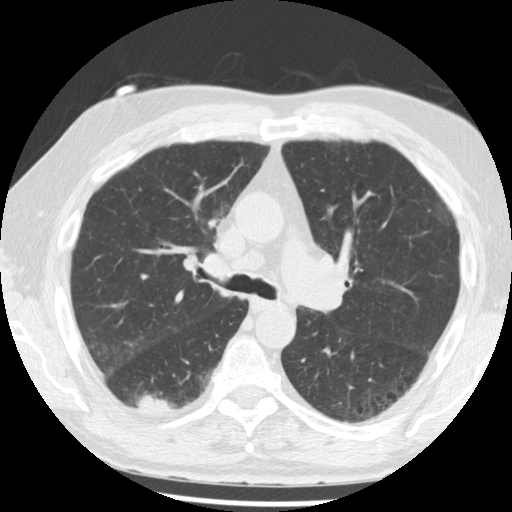
Axial slice from a low-dose chest CT screening exam; third screening round (two years after baseline); lung window (W 1500 / L -600 HU); 2.5 mm slice thickness; slice 134 of 221 in the series. Male participant, aged 68 years at enrolment. Current smoker at enrolment.
Expert-annotated lung lesion, bounding box (x1, y1, x2, y2) in pixels: (124, 378, 184, 424). The screening reader recorded 3 non-calcified nodules or masses ≥4 mm on this exam (right lower lobe, right lower lobe, right lower lobe); which of them this box marks is not recorded. Official screen result: positive, other. Lung cancer was diagnosed 48 days after this screen: squamous cell carcinoma, NOS, right lower lobe, moderately differentiated (G2), stage IB (AJCC 6th edition), 20 mm at pathology.